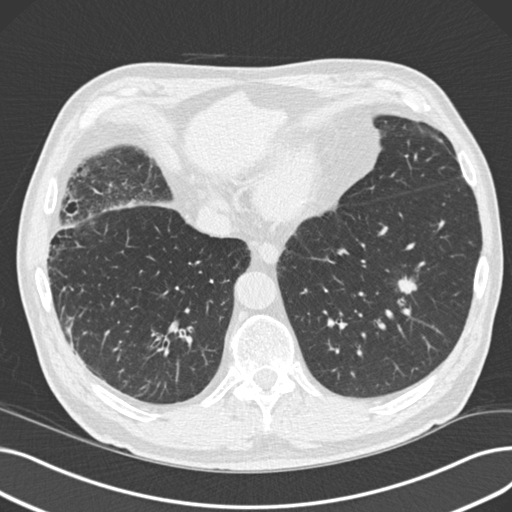
Low-dose screening chest CT, one axial slice; position 39 of 165 along the scan axis; reconstruction kernel B30f; 120 kVp; lung window (W 1500 / L -600 HU); 2 mm slice thickness; 512 × 512 image matrix, field of view 369 × 369 mm.
Outlined on this slice (manually delineated by an expert):
- lesion 1 (tumor, lower lobe of left lung): bounding box <398,278,417,294> (left, top, right, bottom; pixels)